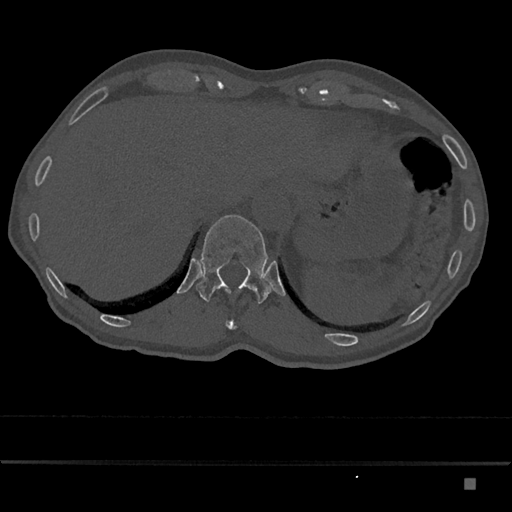
CT including the spine, one axial slice. Slice 627 of 797 in the series (ordered by position). Reconstruction kernel Br40s/3. Bone window (W 1800 / L 400 HU). 512 × 512 image matrix. Male patient, age 72 years. From the clinical record (not read from this slice): primary cancer: prostate.
Annotated regions visible in this slice (semi-automatically segmented with operator editing):
- T11 vertebra: bounding box [x1, y1, x2, y2] px = [226, 320, 237, 330]
- T12 vertebra: [196, 215, 272, 304]